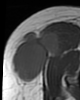
MRI of an extremity soft-tissue mass, one axial slice. Position 27 of 46 along the scan axis. MR volume resampled by the dataset authors to the PET/CT grid (not the native acquisition matrix). 3.27 mm slice thickness. 80 × 100 image matrix, field of view 78 × 98 mm. Female patient. From the clinical record (not read from this slice): histological type: synovial sarcoma; grade: intermediate; site of the primary tumour: right thigh.
Structures marked on this image (expert contour drawn on MRI and transferred to this co-registered scan by the dataset authors):
- gross tumour volume including surrounding oedema: bounding box (x1, y1, x2, y2) in pixels: (12, 28, 63, 84)
- gross tumour volume (mass): (12, 28, 63, 82)